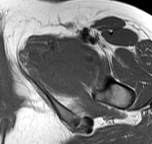
MRI of an extremity soft-tissue mass, one axial slice. Slice 46 of 57 in the series (ordered by position). MR volume resampled by the dataset authors to the PET/CT grid (not the native acquisition matrix). 3.27 mm slice thickness. 152 × 144 image matrix, field of view 148 × 141 mm. Female patient. Case-level facts recorded for this patient, not image findings: histological type: pleiomorphic leiomyosarcoma; grade: intermediate; site of the primary tumour: left thigh.
Annotated regions visible in this slice (expert contour drawn on MRI and transferred to this co-registered scan by the dataset authors):
- gross tumour volume including surrounding oedema: bounding box [x1, y1, x2, y2] px = [25, 37, 90, 82]
- gross tumour volume (mass): [47, 42, 87, 81]